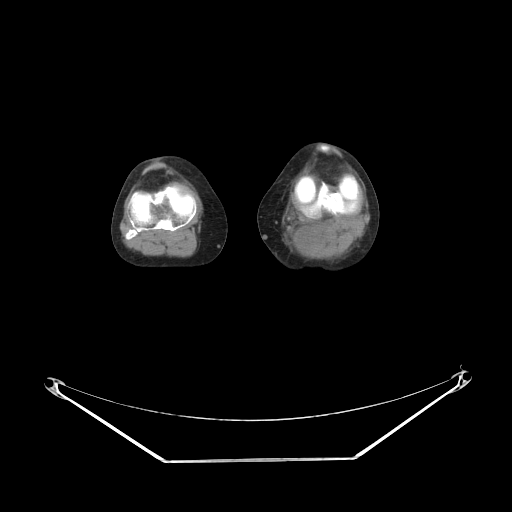
CT of an extremity soft-tissue mass (from a PET/CT study), one axial slice. Position 164 of 223 along the scan axis. Reconstruction kernel STANDARD. 140 kVp. Soft-tissue window (W 400 / L 40 HU). 512 × 512 image matrix, field of view 500 × 500 mm. Female patient. From the clinical record (not read from this slice): histological type: extraskeletal high grade osteogenic sarcoma; grade: high; site of the primary tumour: left calf.
Annotated regions visible in this slice (expert contour drawn on MRI and transferred to this co-registered scan by the dataset authors):
- gross tumour volume (mass): bounding box (x1, y1, x2, y2) in pixels: (297, 231, 316, 250)